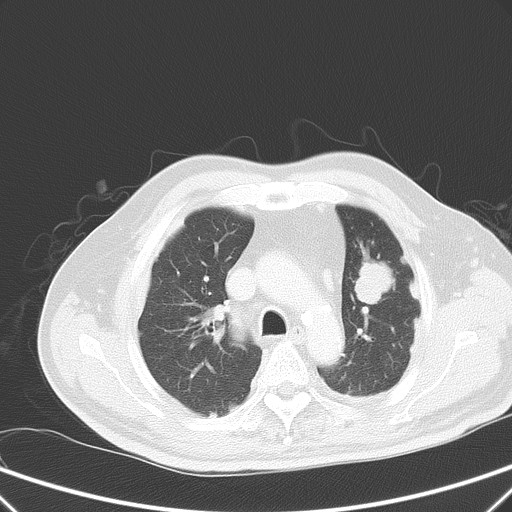
Chest CT, one axial slice; position 42 of 59 along the scan axis; intravenous contrast given; lung window (W 1500 / L -600 HU); 512 × 512 image matrix. Male patient, age 66 years. From the clinical record (not read from this slice): clinical TNM (as recorded): T1c N3 M1a.
Outlined on this slice (rectangle marked by the reading radiologist):
- lung tumour (recorded histology: squamous cell carcinoma): bounding box <353,257,402,307> (left, top, right, bottom; pixels)